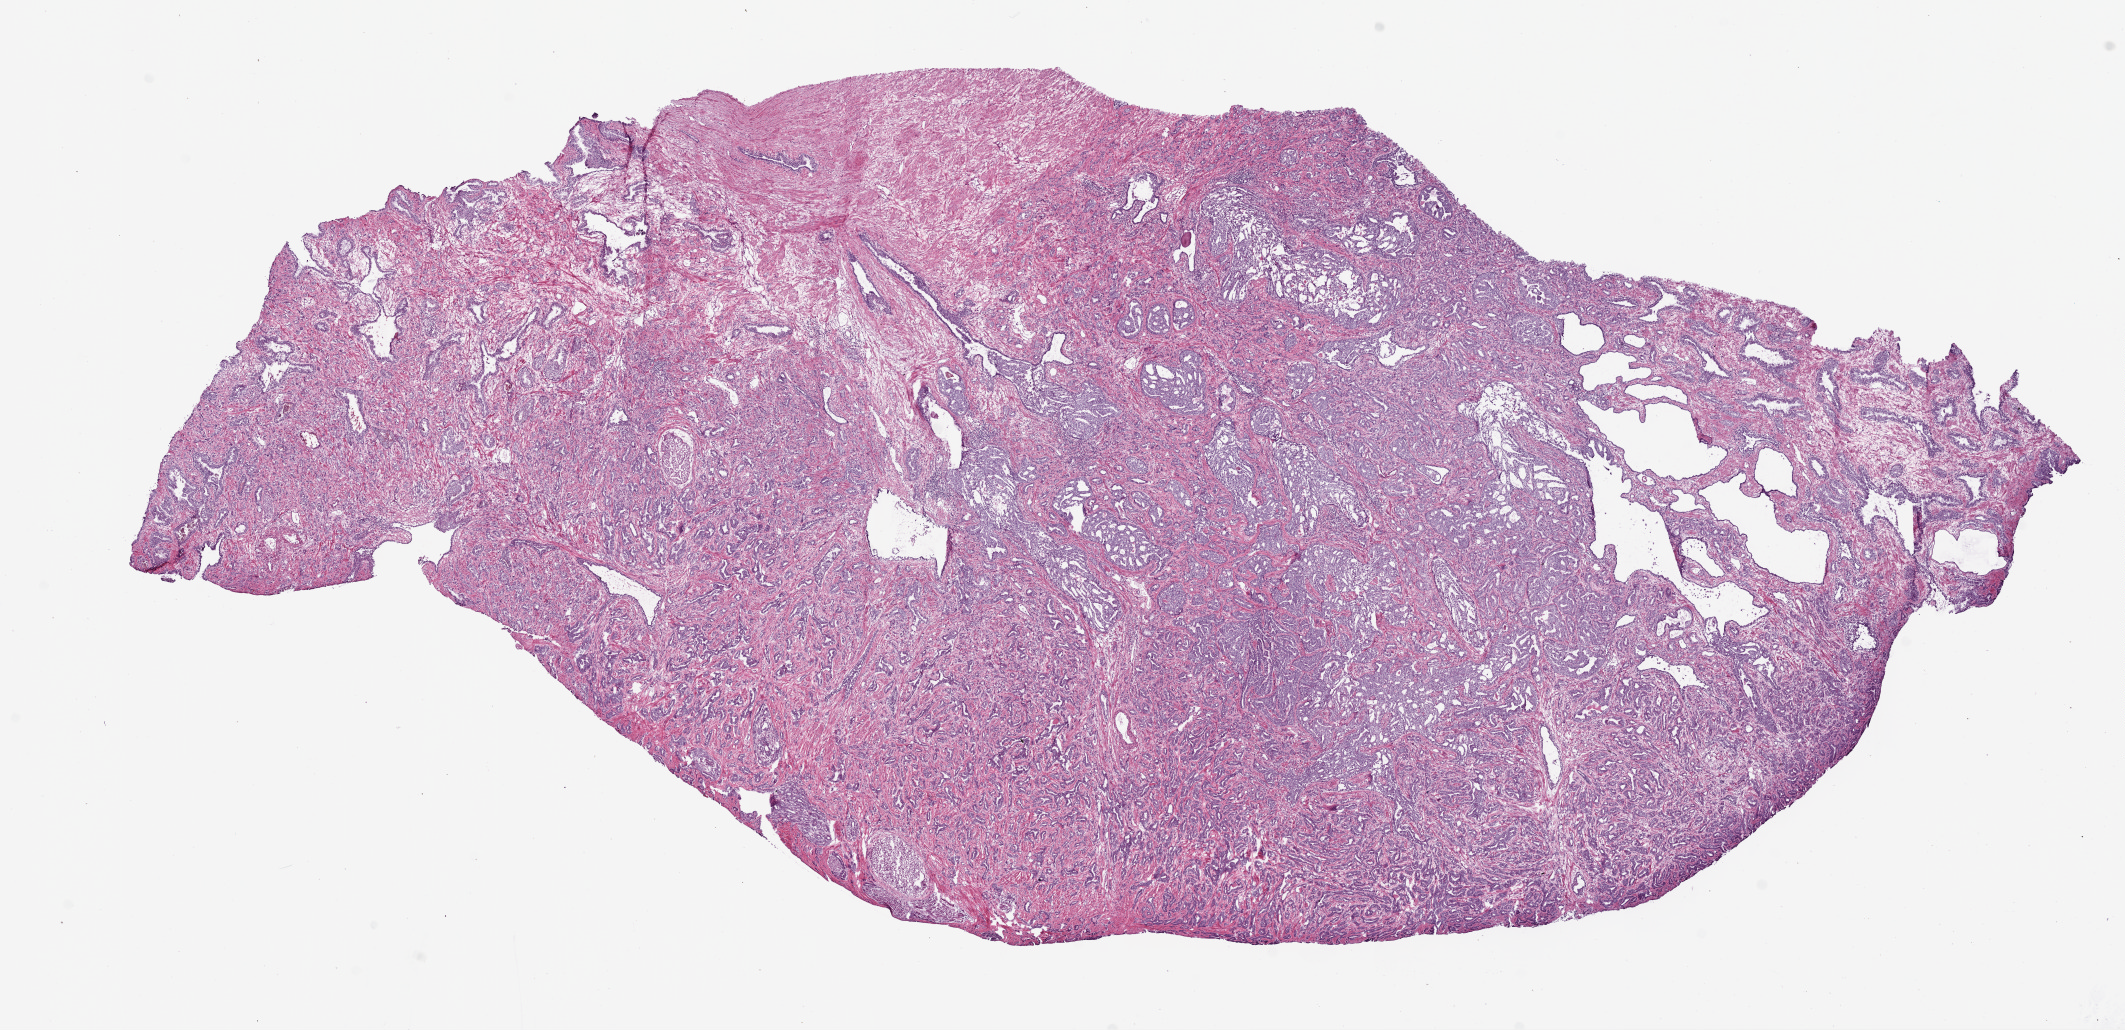
H&E-stained whole-slide image — shown as a low-resolution overview of the whole scanned area (about 17.1 x 8.3 mm, acquisition: 20x scan). Frozen section from the bottom of the tissue portion. Prostate, primary tumour sample. Male patient; age at initial diagnosis 69 years. Gleason score: 7 (4+3). Composition of this section per pathologist review: tumour cells 70%, tumour nuclei 75%, normal cells 10%, stromal cells 20%, necrosis 0%. Infiltration values recorded for this section: lymphocyte infiltration 0%, monocyte infiltration 0%, neutrophil infiltration 0%.
* laterality: bilateral
* diagnosis: Acinar cell carcinoma (prostate gland)